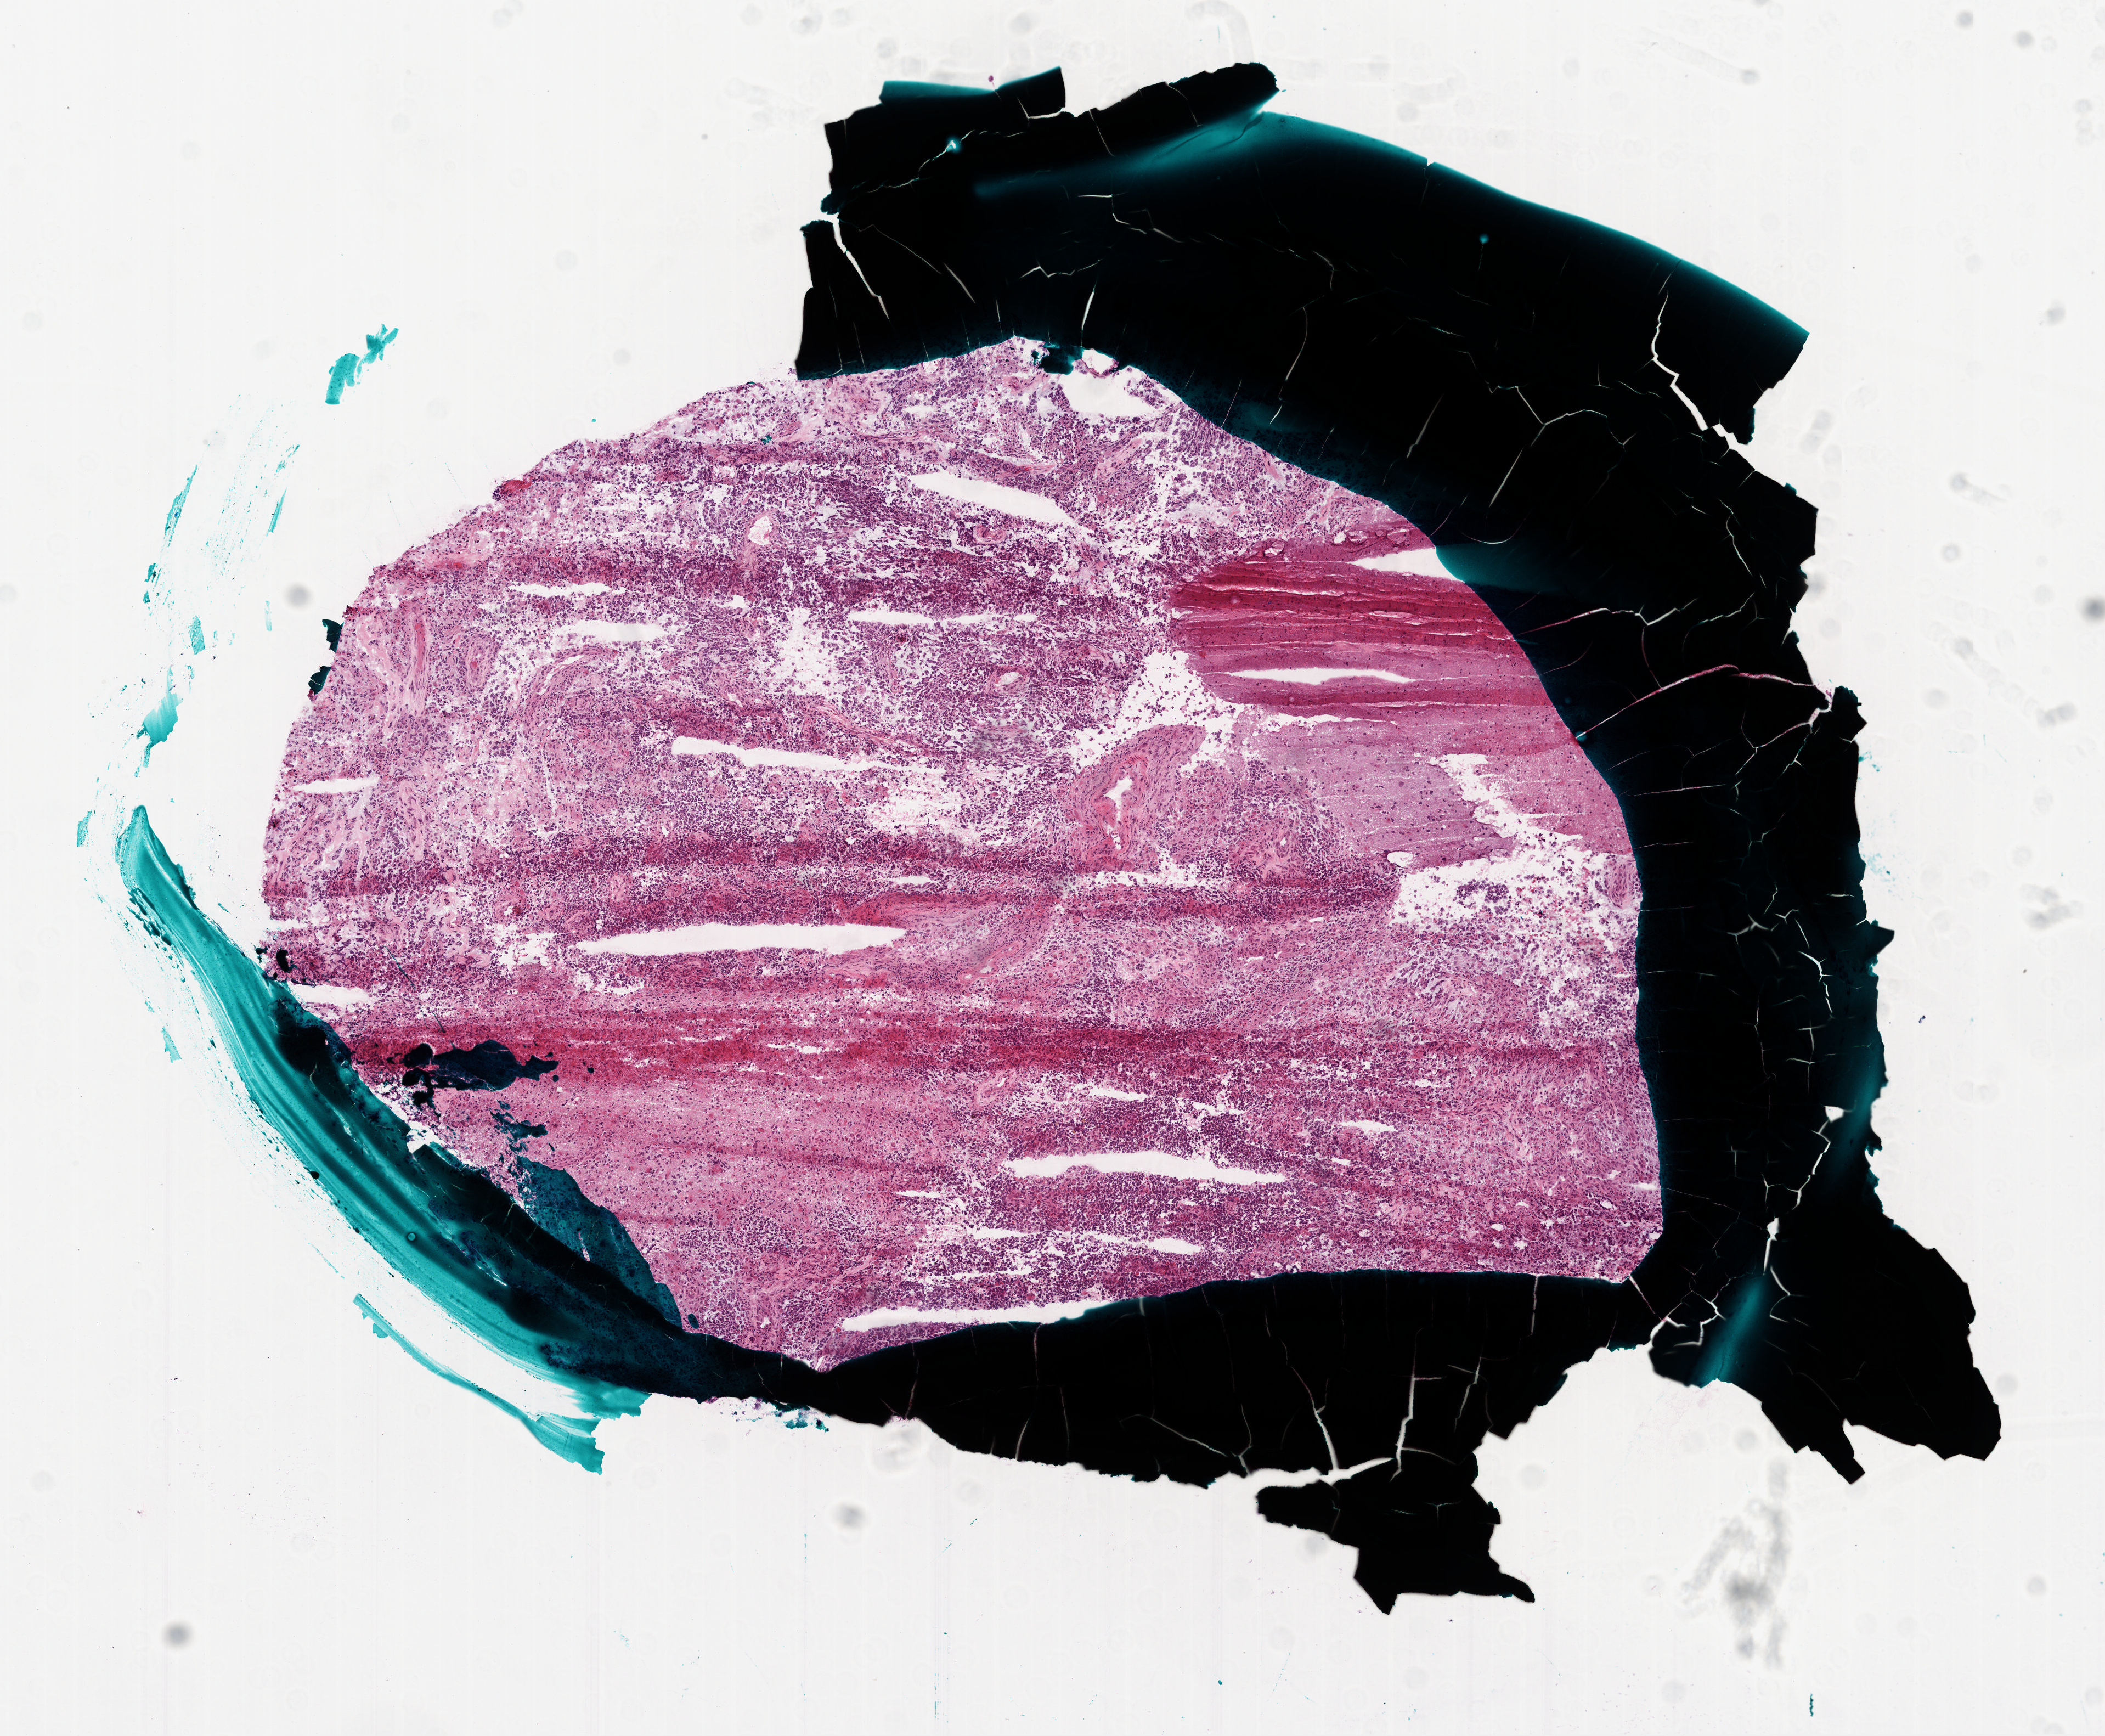
Hematoxylin and eosin (H&E) stained whole-slide image — low-resolution overview of the scanned area, about 7.7 x 6.4 mm (from a 20x scan). Frozen section. Primary tumour sample from the brain. Male, age 64 years at initial diagnosis.
Diagnosis: Glioblastoma.